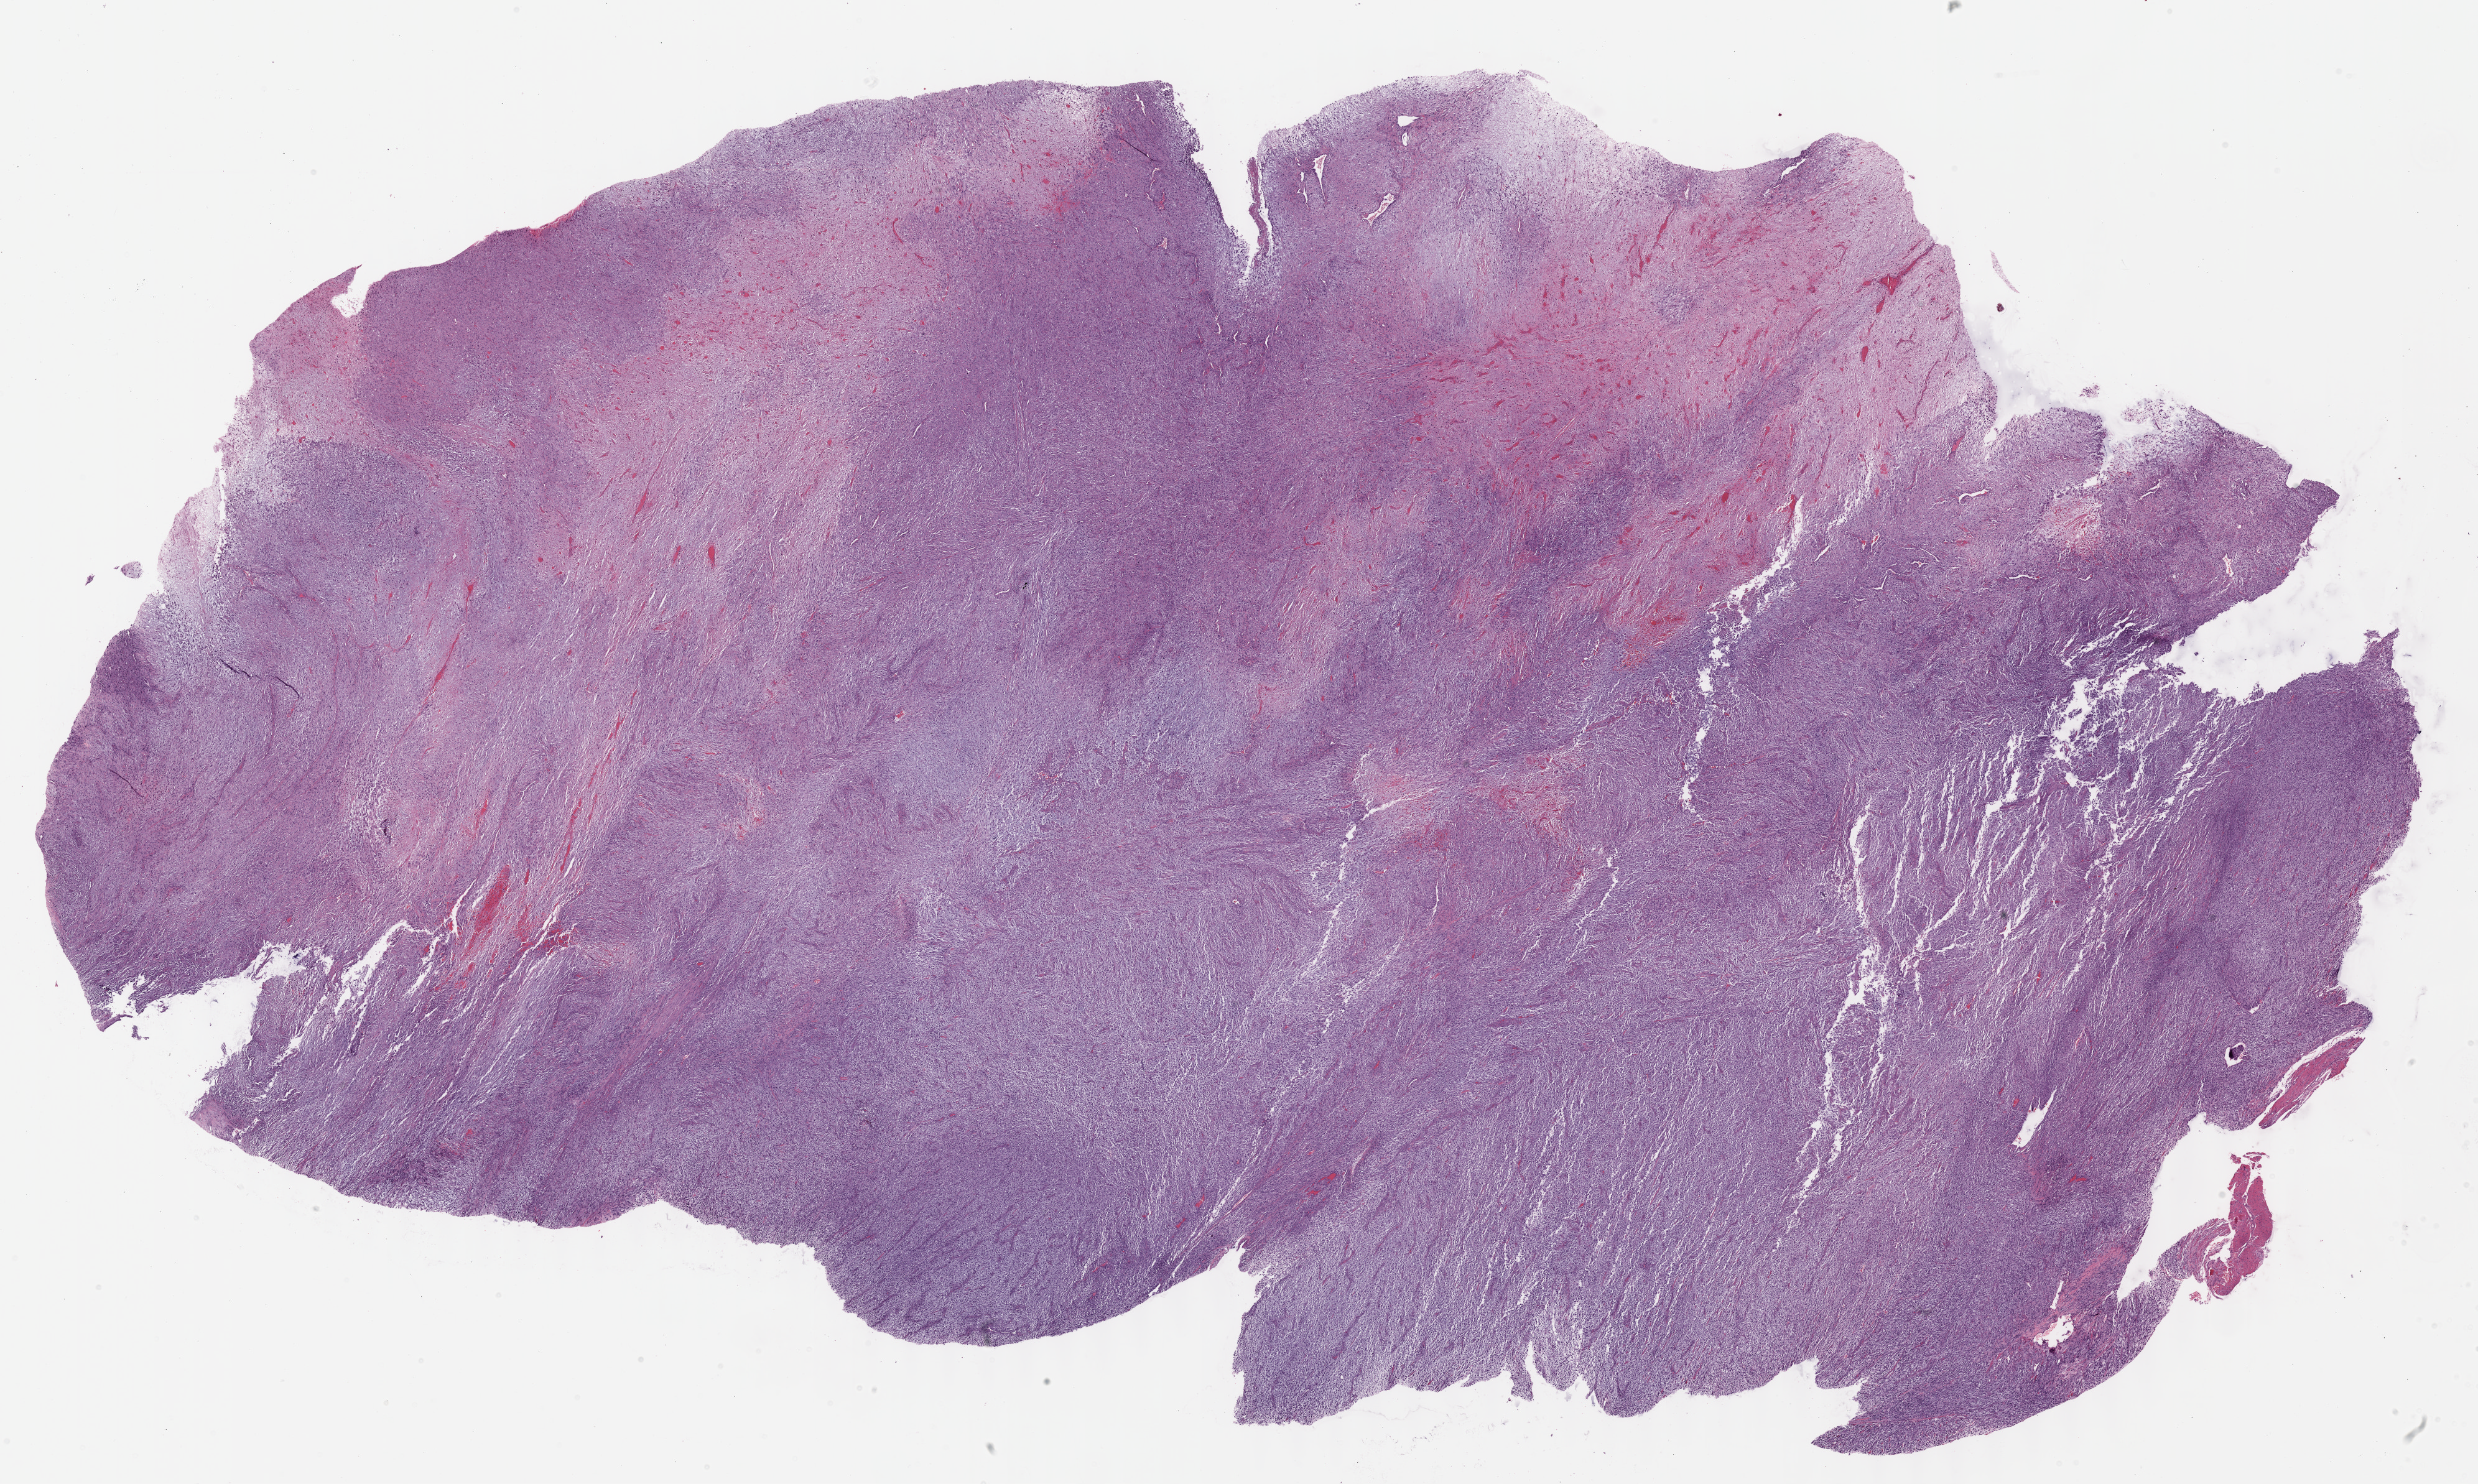
Whole-slide histology image, H&E-stained — low-resolution overview of the scanned area, about 32.2 x 19.3 mm (slide scanned at 40x); formalin-fixed paraffin-embedded (FFPE) diagnostic section; primary tumour sample from the connective, subcutaneous and other soft tissues. Female patient.
Diagnosis: Undifferentiated sarcoma (connective, subcutaneous and other soft tissues of lower limb and hip).